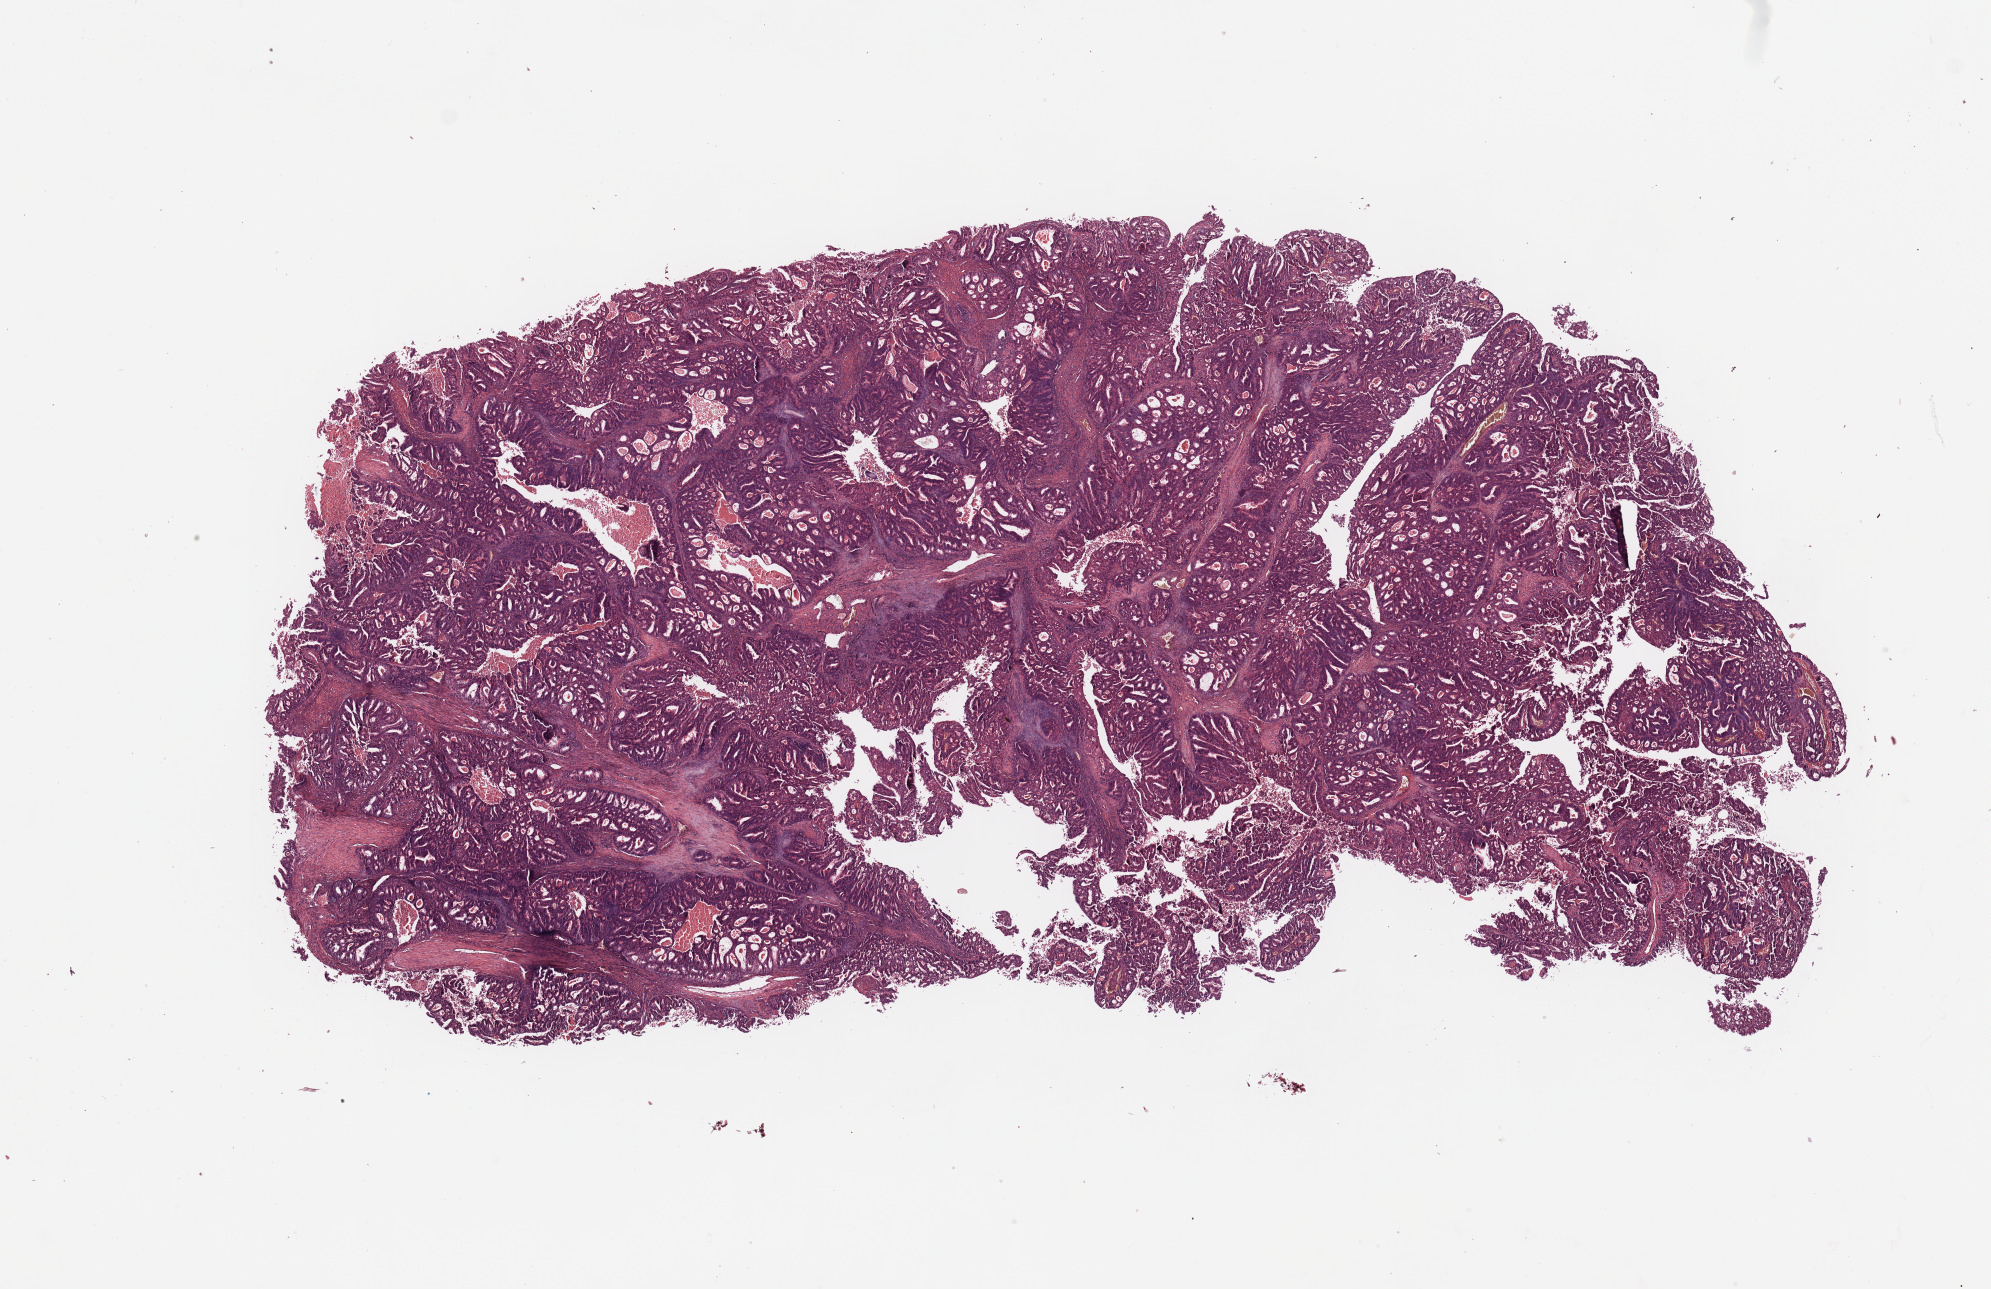
Digitized H&E-stained tissue section (whole slide) — low-resolution overview of the scanned area, about 15.8 x 10.2 mm (slide scanned at 20x); tumour tissue sample, sampled site: uterus. Patient: female, age 73 years. Histologic grade: G2 (moderately differentiated). Pathologist review of this section (percent, as recorded): tumour nuclei 90%, necrosis 5%.
Histologic diagnosis: Endometrioid adenocarcinoma, NOS. AJCC pathologic stage: I.